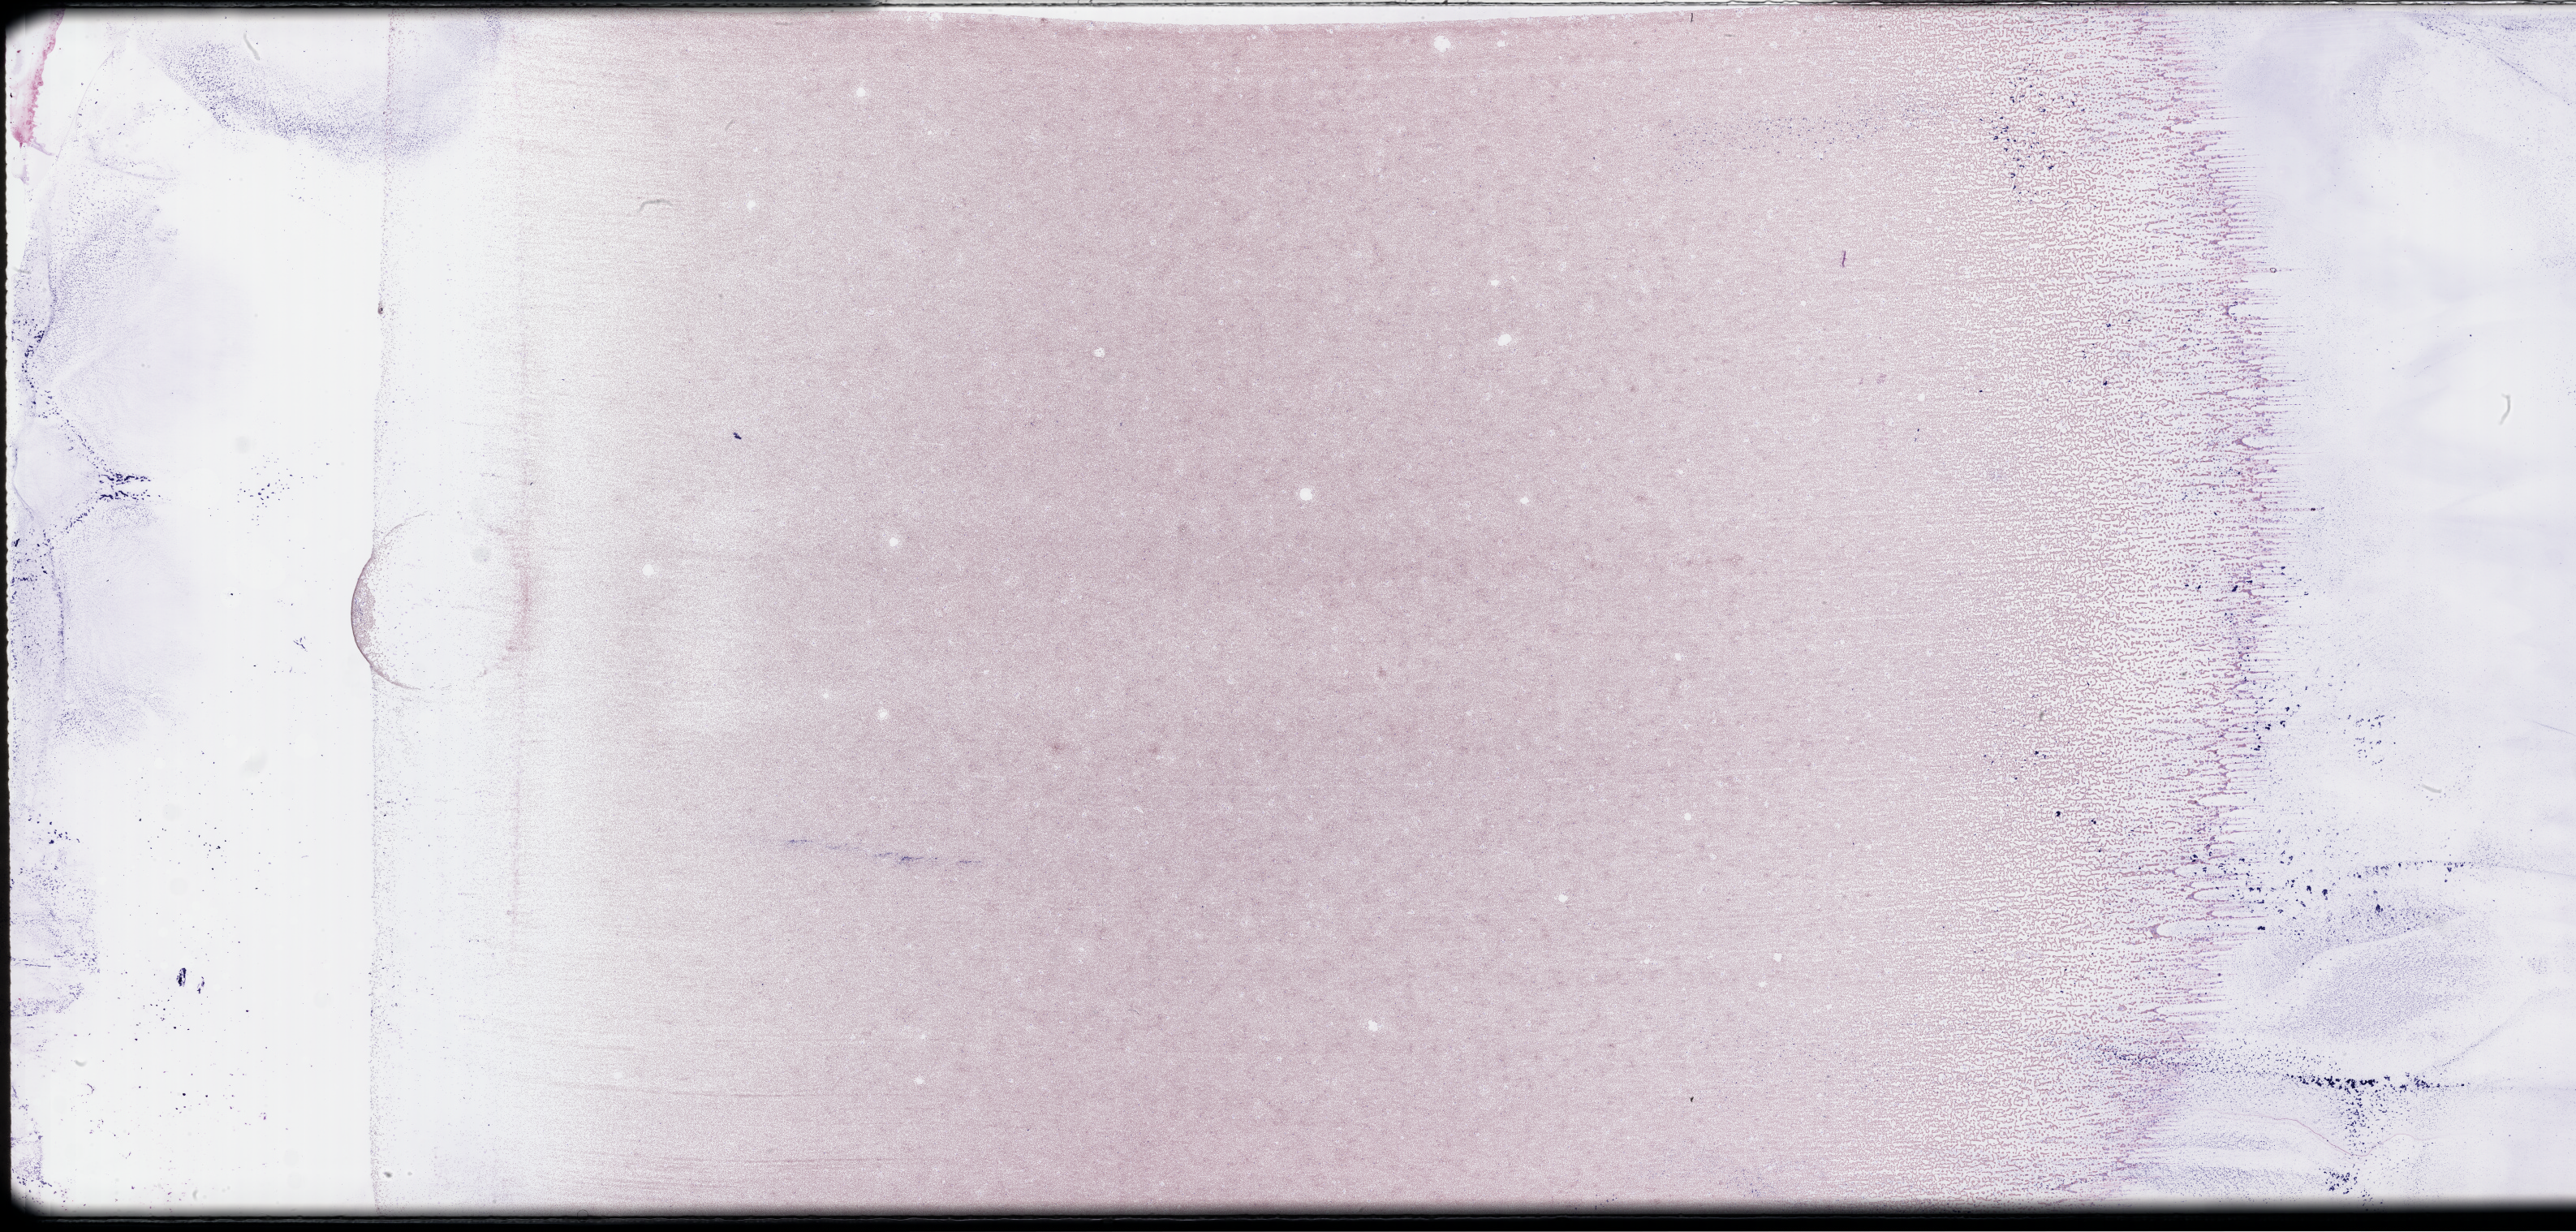
Wright–Giemsa-stained bone marrow smear, whole-slide image — low-resolution overview of the scanned area, about 51.3 x 24.5 mm. EDTA-anticoagulated smear. Collected at baseline (before treatment). Patient sex: male.
From a patient with: Plasma Cell Myeloma.